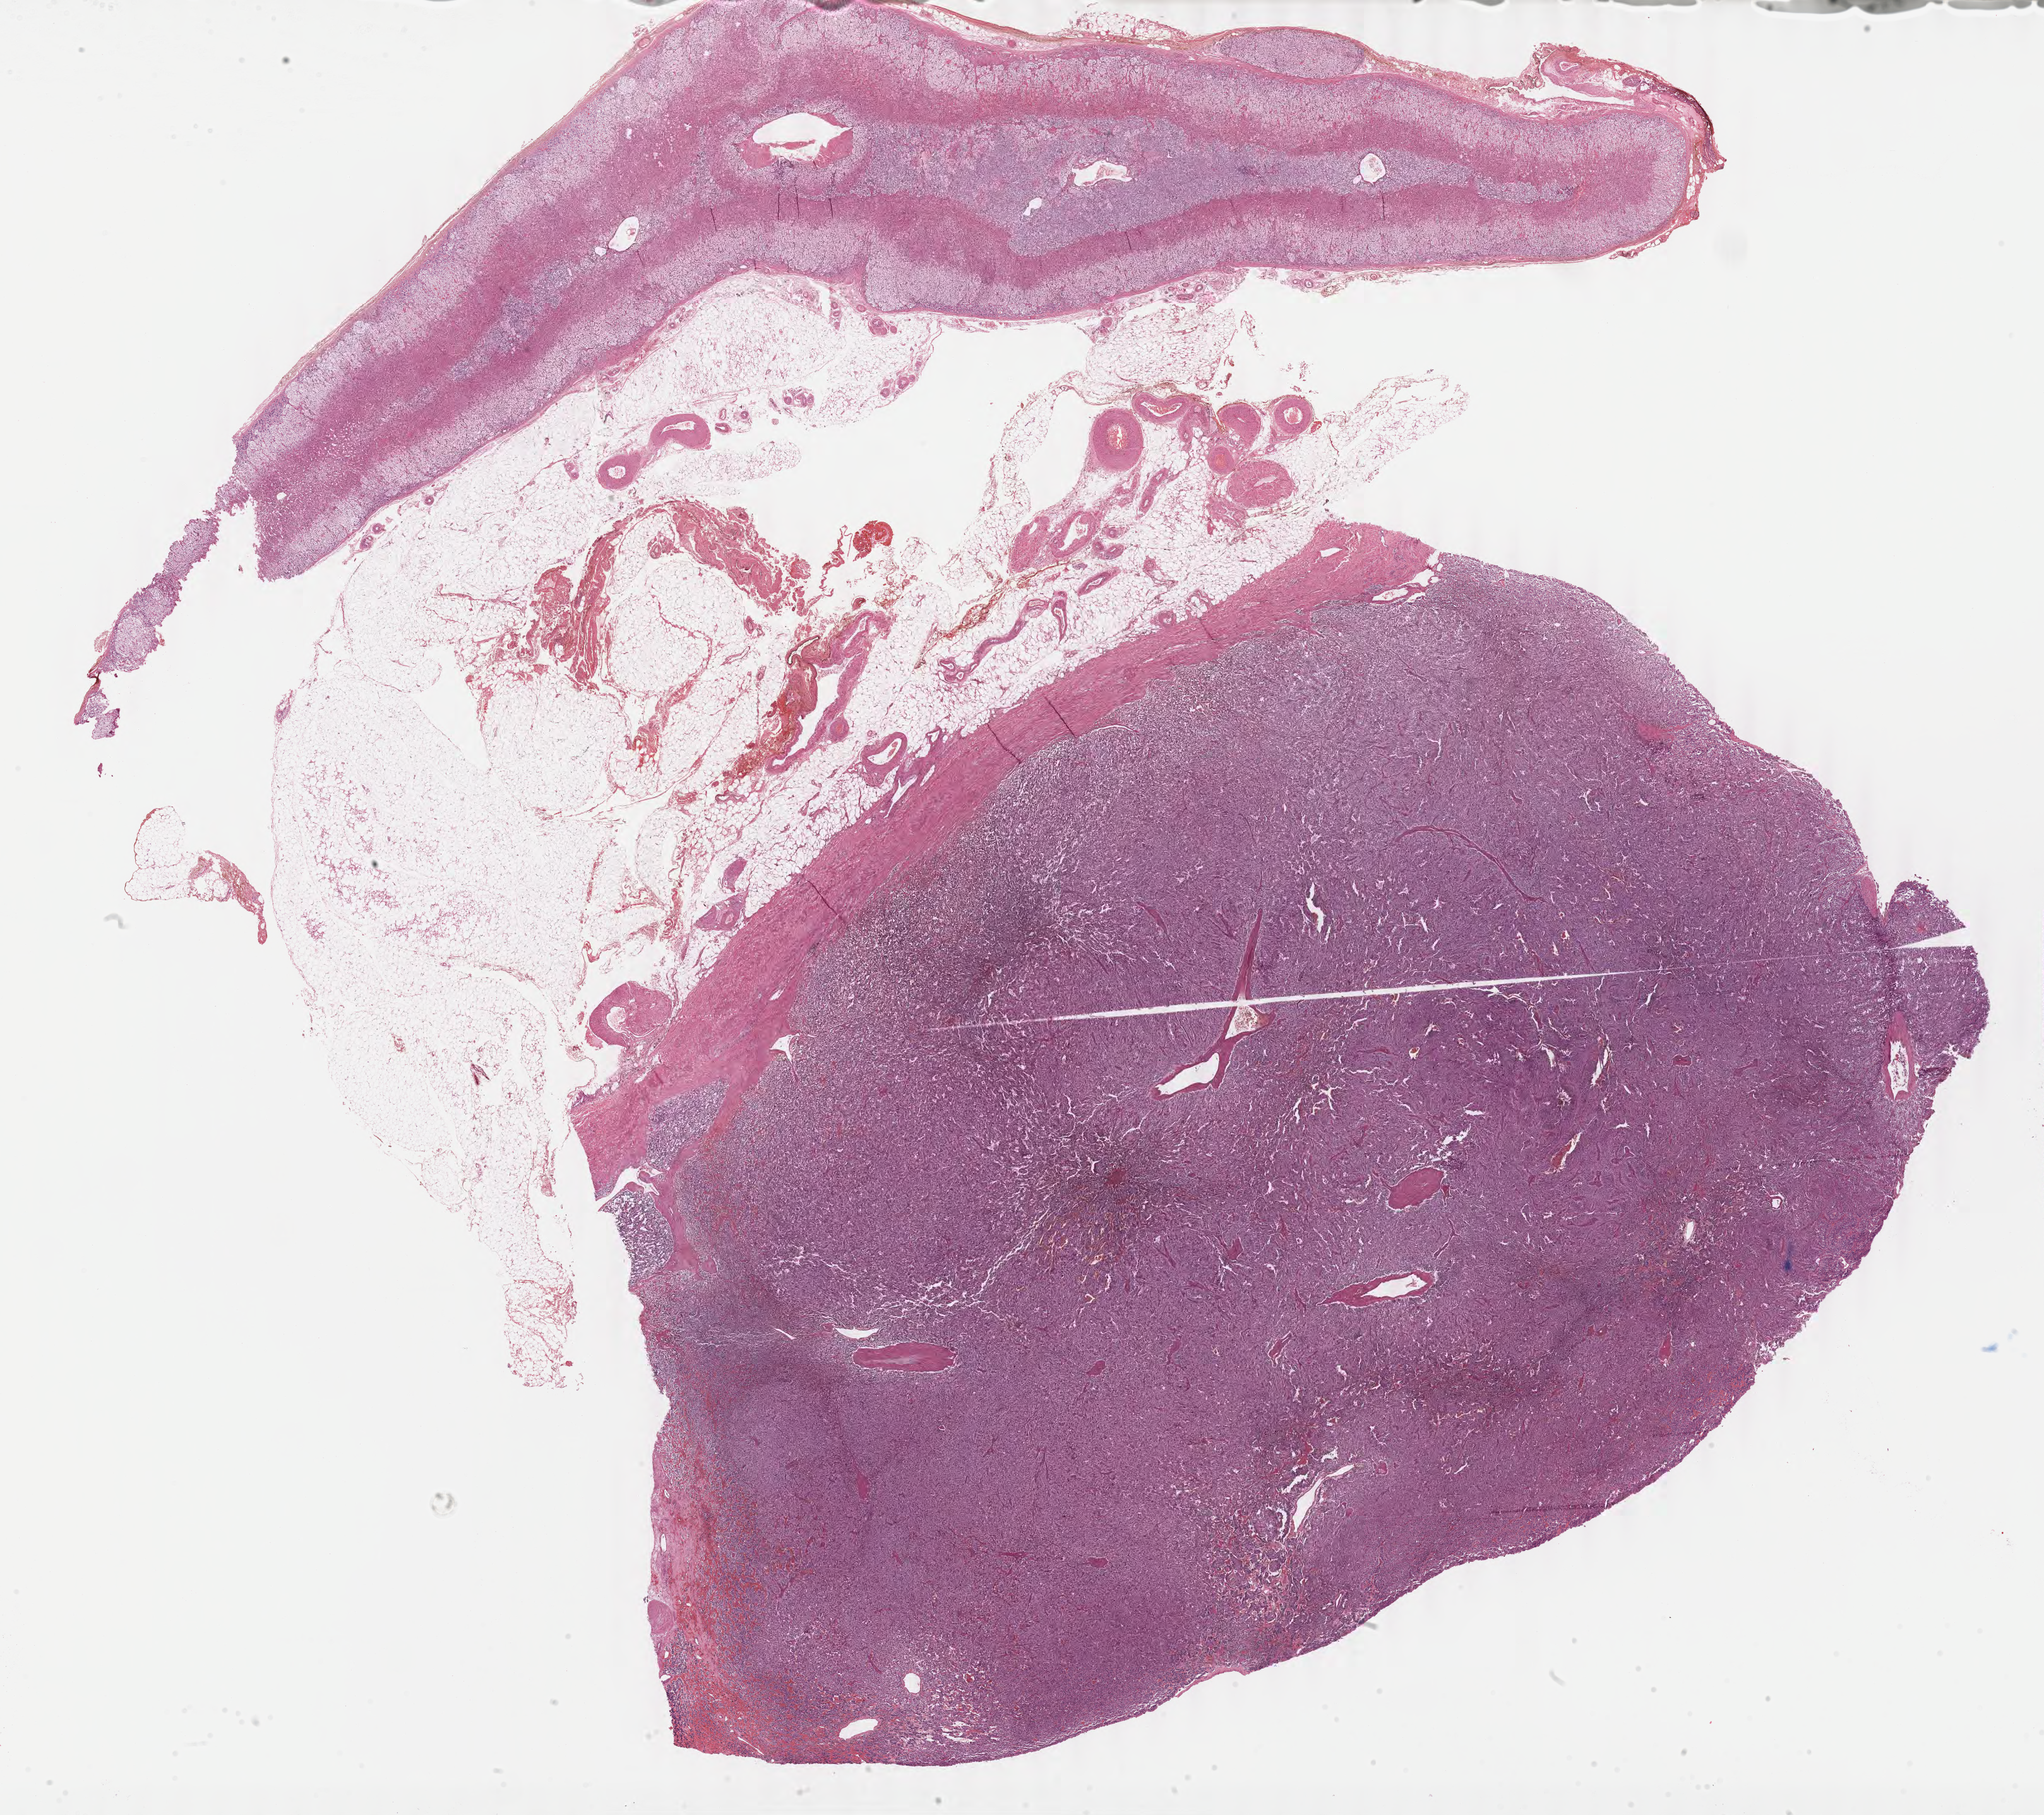
Whole-slide histology image, Hematoxylin and eosin (H&E) stained, whole scanned area (about 25.6 x 22.7 mm, from a 40x scan) shown as a low-resolution overview; formalin-fixed paraffin-embedded (FFPE) diagnostic section; sample: primary tumour, retroperitoneum and peritoneum. Female, age 35 years at initial diagnosis.
Diagnosis: Extra-adrenal paraganglioma, NOS (retroperitoneum).